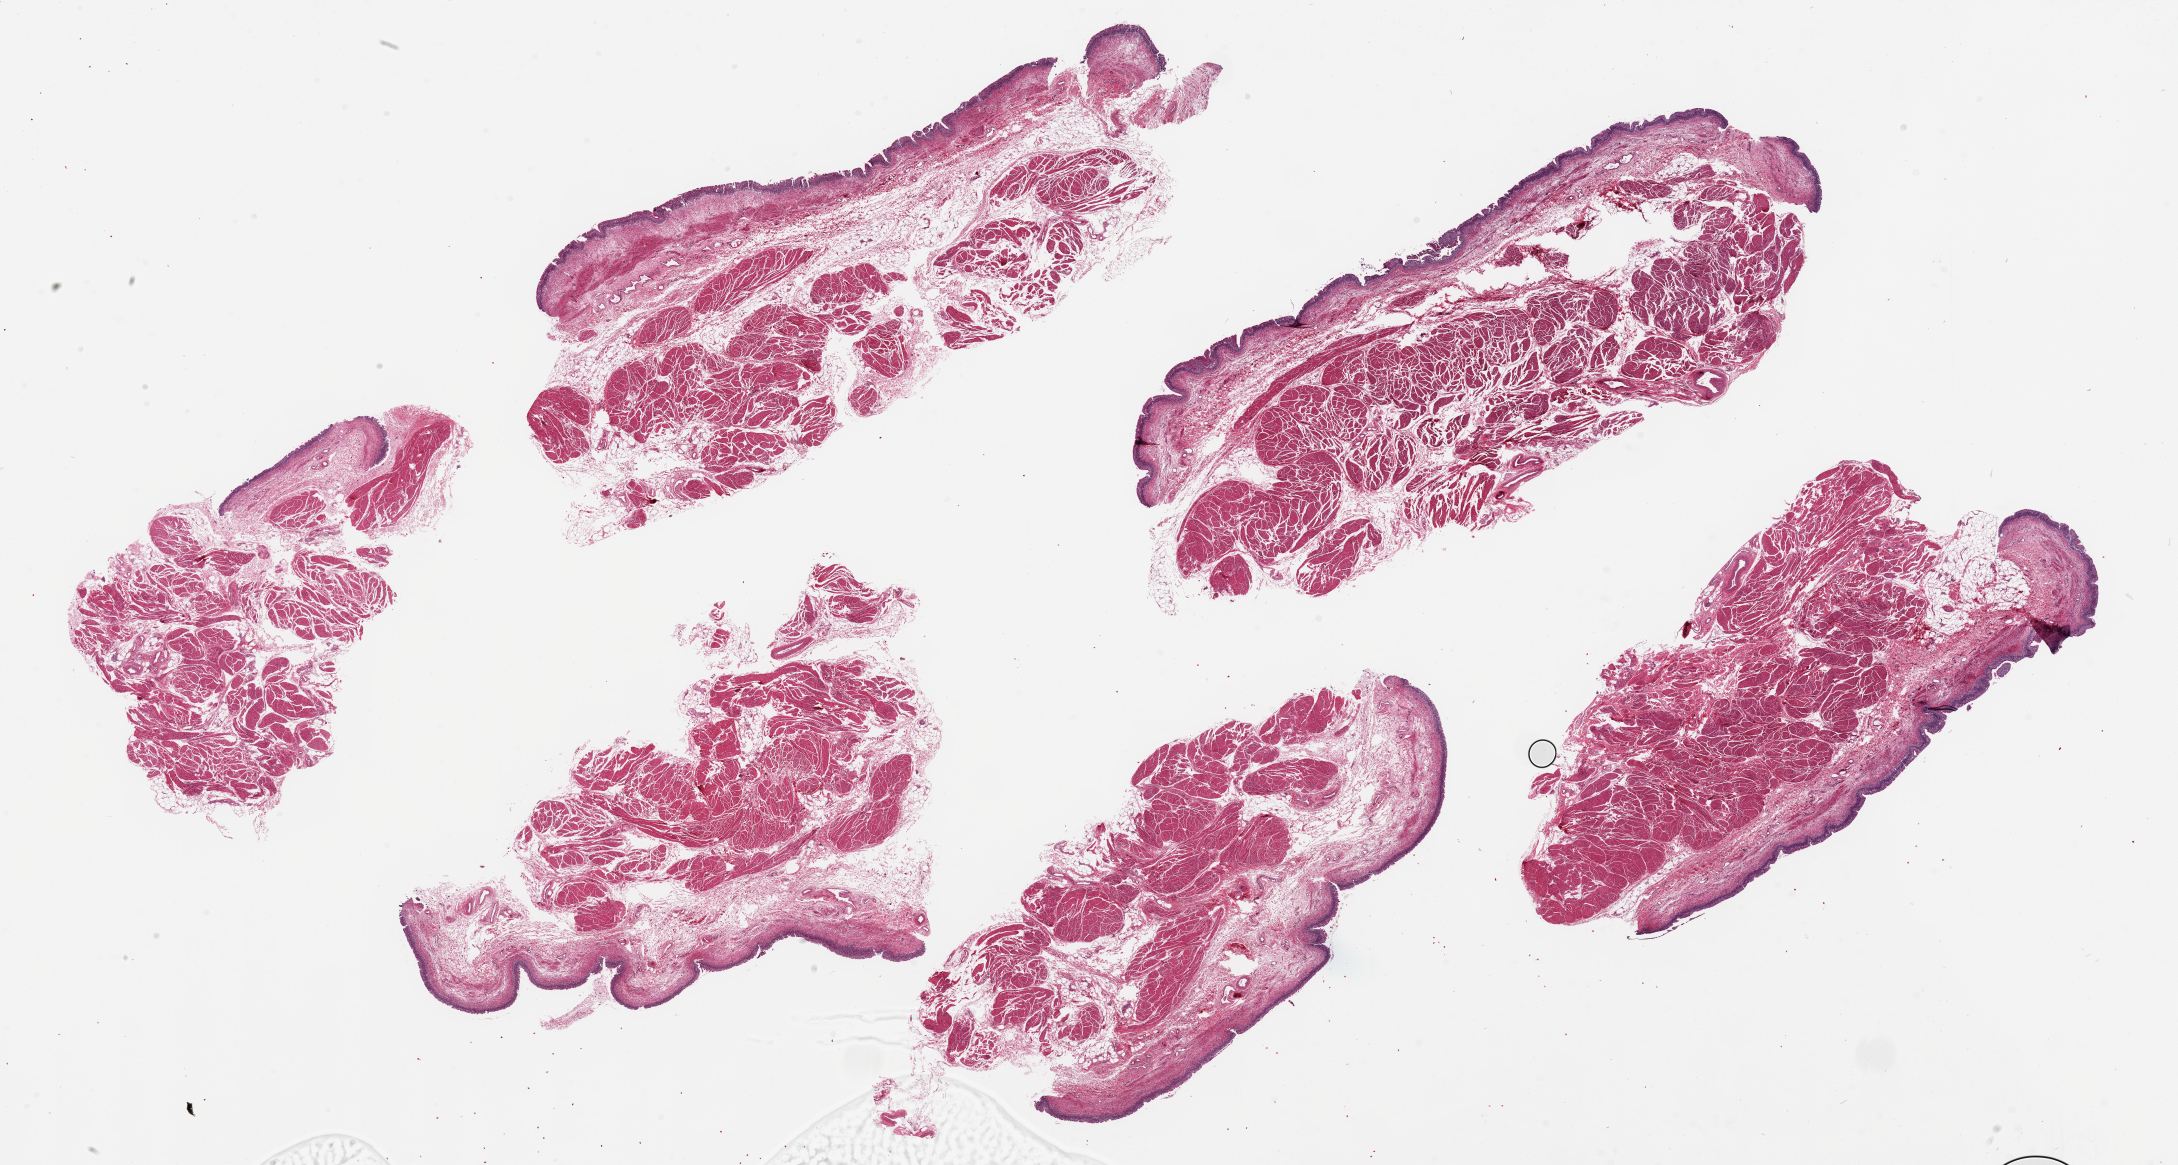
Whole-slide image, hematoxylin and eosin (H&E) stain, low-resolution overview of the scanned area, about 34.5 x 18.4 mm (acquisition: 20x scan); PAXgene-fixed, paraffin-embedded tissue; section of urinary bladder (target tissue); donor tissue sample. Donor: female.
Reviewer comment on this tissue sample: 6 pieces ~10x4mm. Urothelium unusually well-preserved, ~3% of thickness.